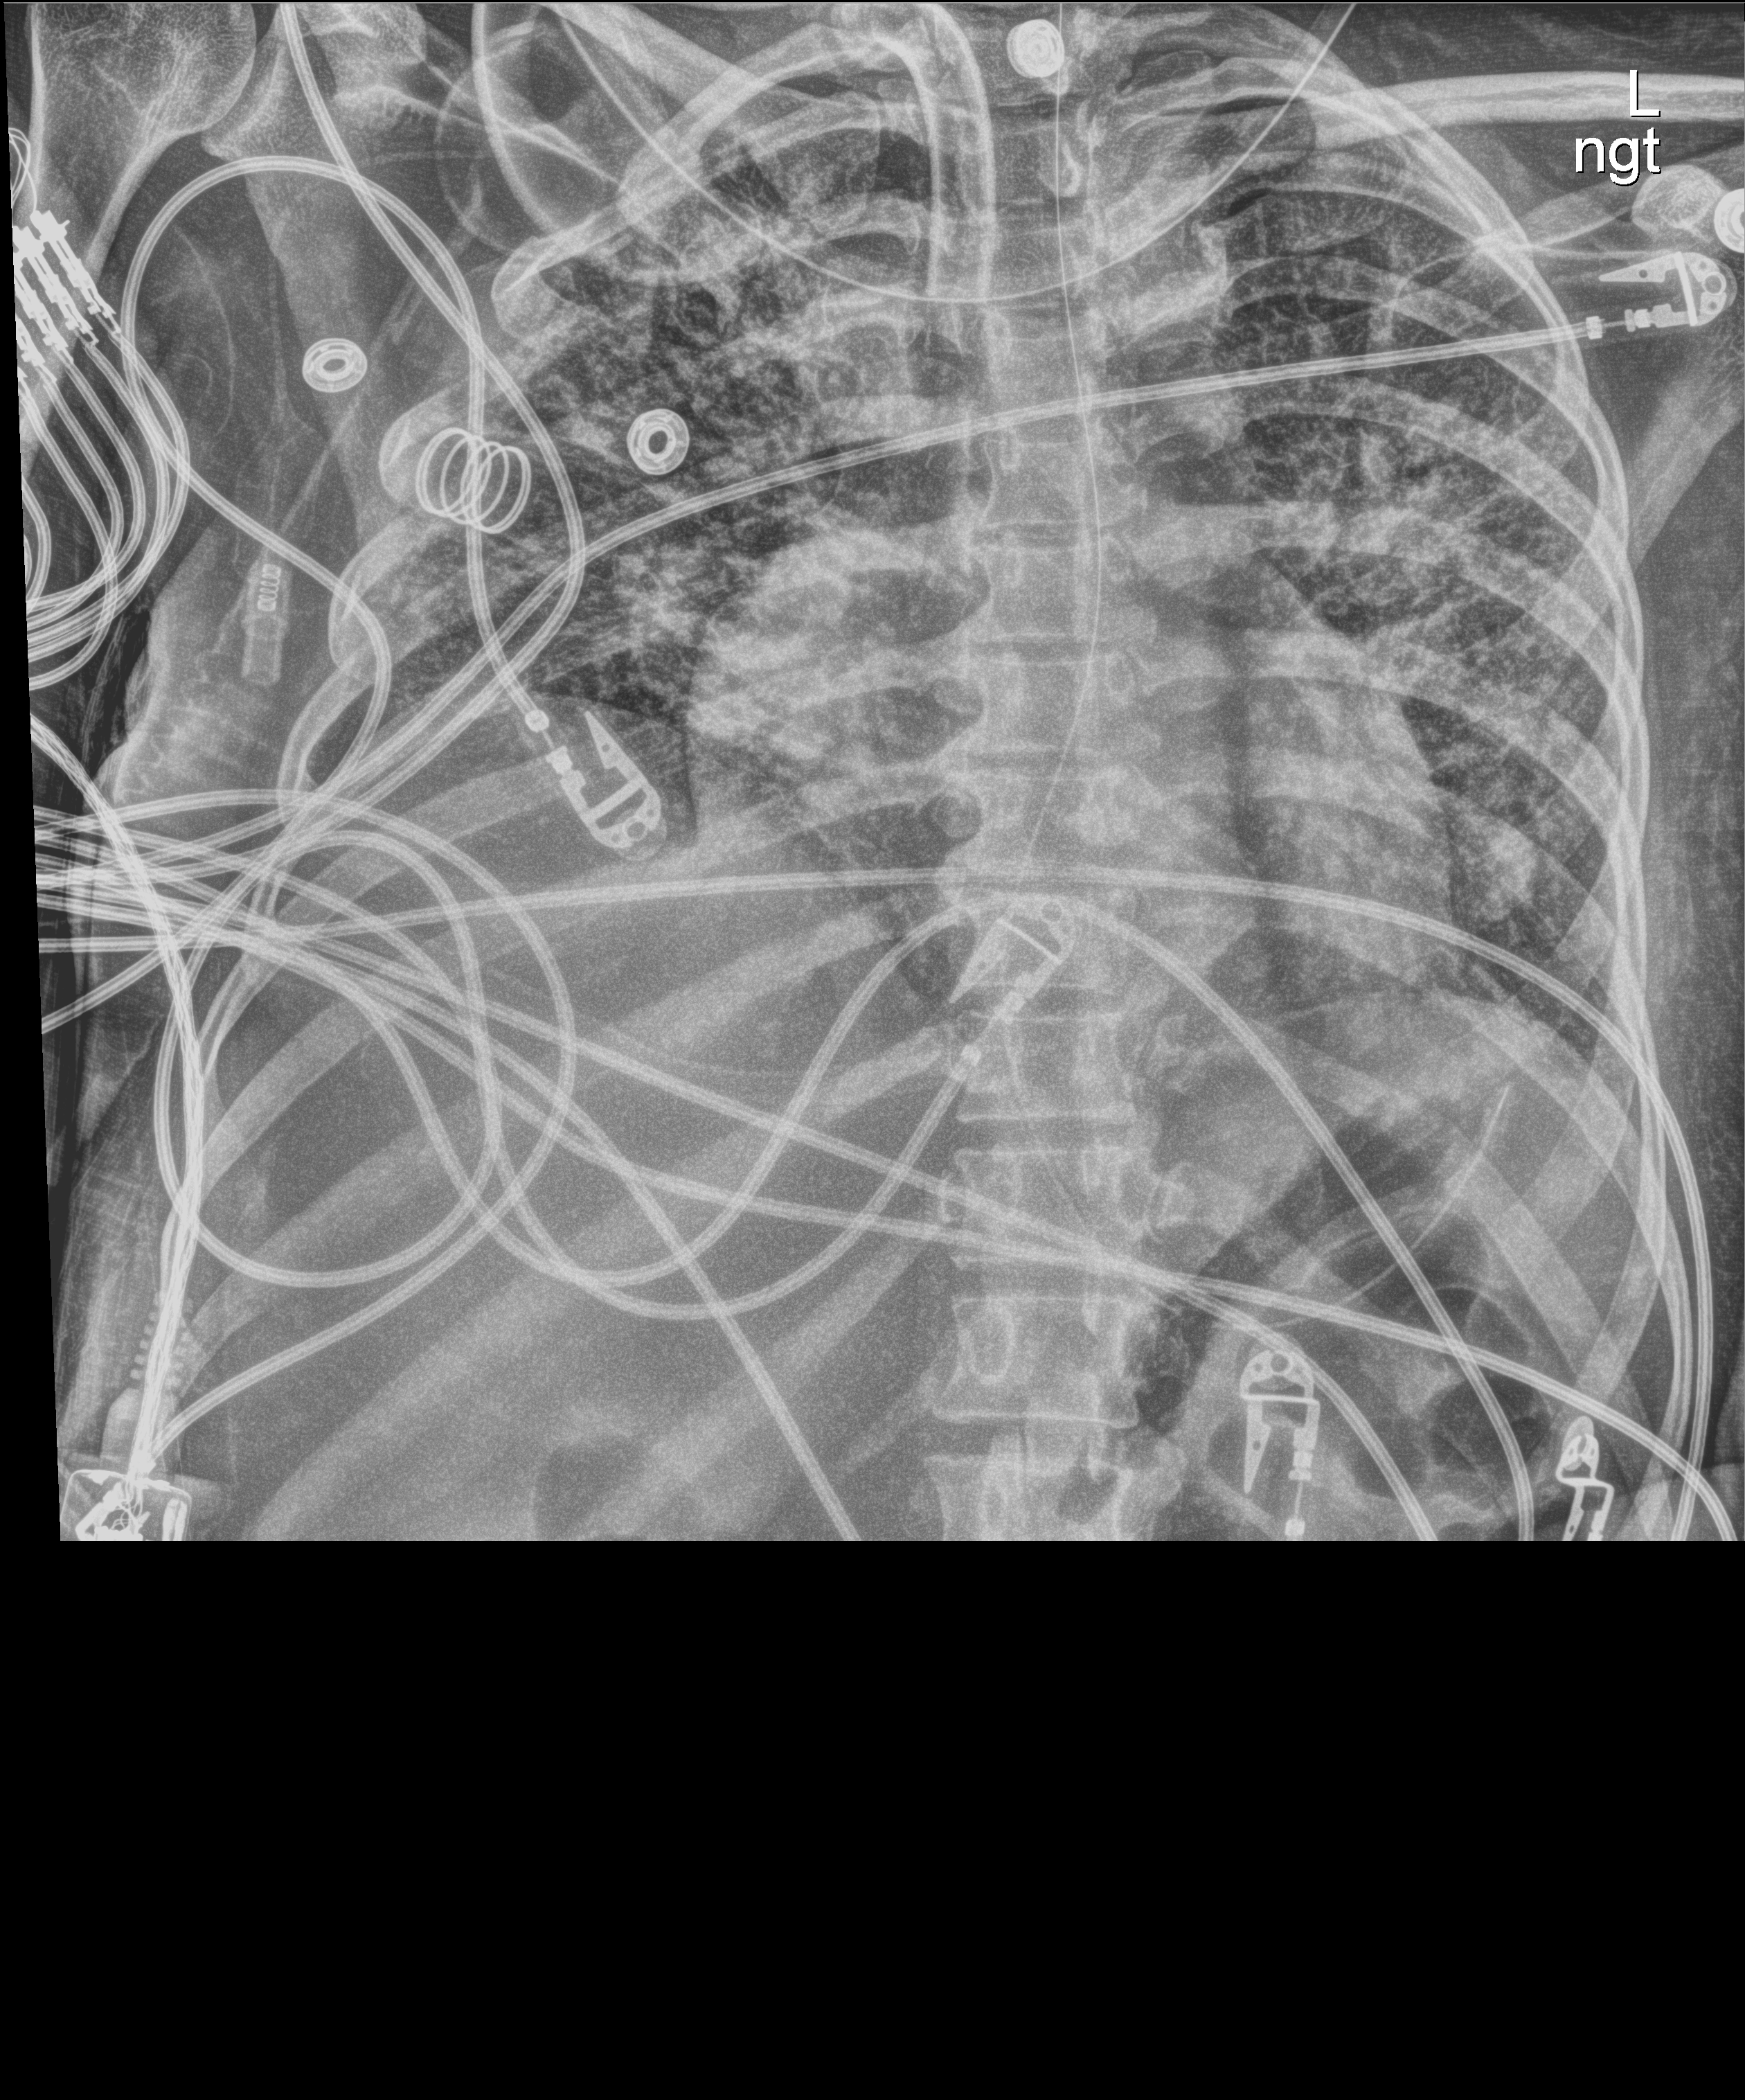
Chest X-ray, anteroposterior (AP) projection. Female patient hospitalised with COVID-19, age 18–59 years.
From the hospital-stay record, not from the radiograph (when in the stay this image was taken is not recorded):
- other chronic lung disease (admission record): no
- admitted to intensive care during this hospital stay: yes
- chronic kidney disease (admission record): no